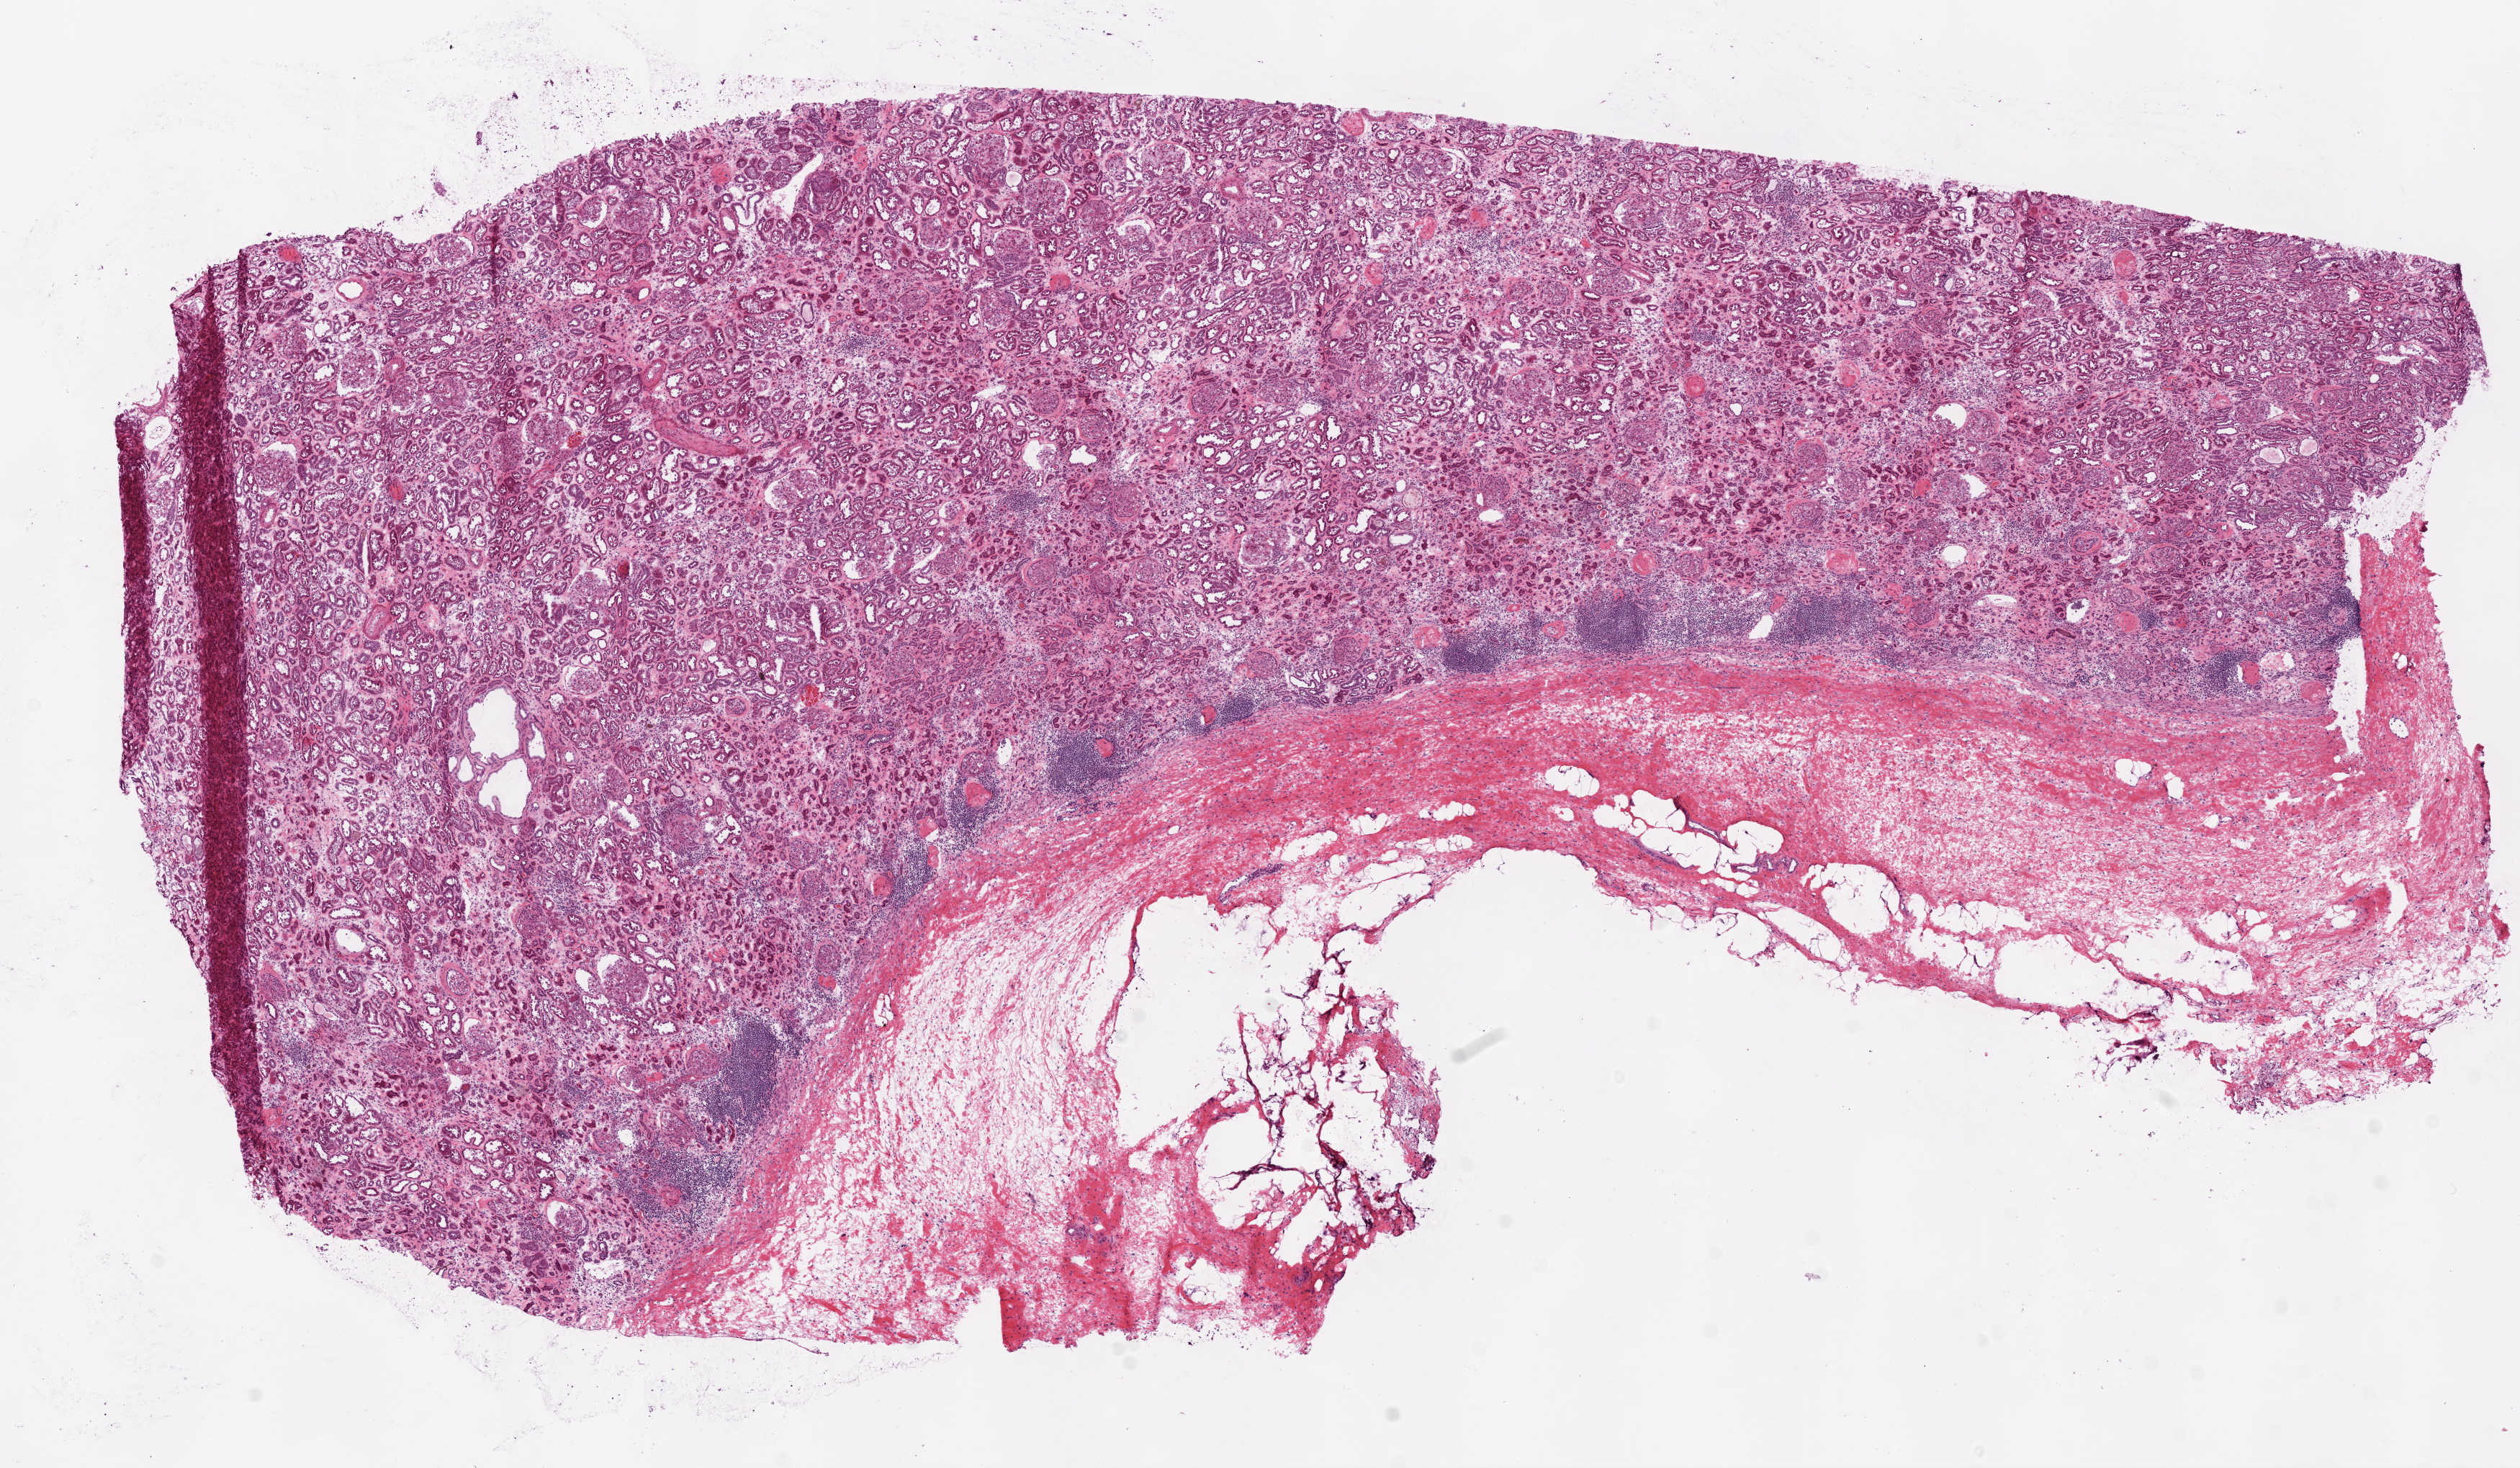
Hematoxylin and eosin (H&E) stained whole-slide image, whole scanned area (about 14.0 x 8.2 mm, acquisition: 20x scan) shown as a low-resolution overview. Frozen section from the top of the tissue portion. Kidney, solid tissue normal (non-tumour tissue) sample. Male, age 56 years at initial diagnosis.
This section: solid tissue normal sample (biorepository sample class). Patient diagnosis: Papillary adenocarcinoma, NOS.